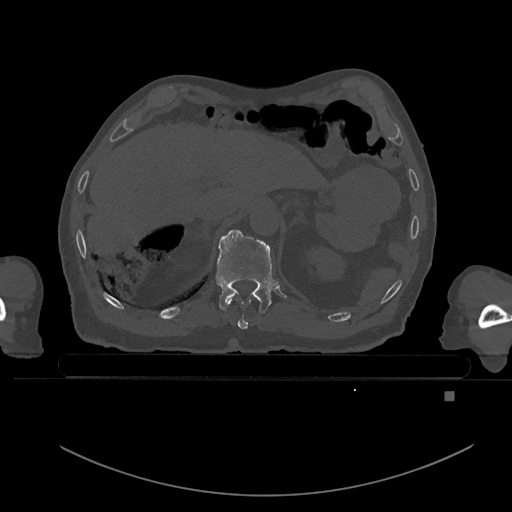
CT including the spine, one axial slice. Slice 46 of 969 in the series (ordered by position). Bone window (W 1800 / L 400 HU). 0.5 mm slice thickness. 512 × 512 image matrix, field of view 456 × 456 mm. Patient: male, 82 years. From the clinical record (not read from this slice): primary cancer: prostate.
Annotated regions visible in this slice (semi-automatically segmented with operator editing):
- T10 vertebra: bounding box <227,299,252,330> (left, top, right, bottom; pixels)
- T11 vertebra: <217,229,278,314>